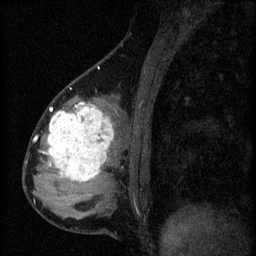
Breast MRI (dynamic contrast-enhanced), one sagittal slice; position 20 of 60 along the scan axis; 3 images stored at this slice position (order not interpretable as contrast timing); 1.5 T; TE 4.2 ms, TR 8.2 ms; 256 × 256 image matrix, field of view 180 × 180 mm. Female patient, age 37 years.
Annotated regions visible in this slice (semi-automatically segmented with operator editing):
- analysis volume of interest (the breast-tissue region the enhancement analysis was run in; not a lesion): bounding box (x1, y1, x2, y2) in pixels: (44, 100, 119, 197)
- tumour enhancement mask (voxels above the 70 % enhancement threshold inside the analysis volume of interest): (48, 102, 115, 183)